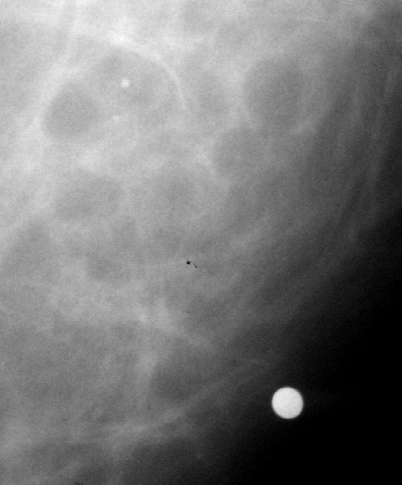
Crop from a digitized film mammogram around one marked abnormality, left breast, MLO view, BI-RADS breast density category 1 (scale 1–4).
Mass, shape focal asymmetric density, margins ill defined; BI-RADS assessment category 3; pathology result (as recorded, not read from the image): benign.